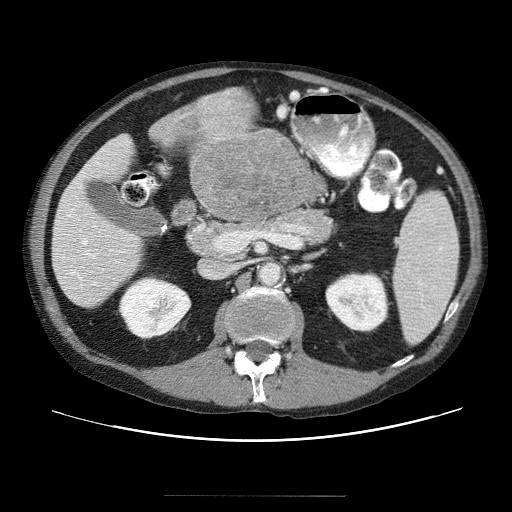
Contrast-enhanced abdominal CT (liver protocol), one axial slice; slice 13 of 69 in the series (ordered by position); 120 kVp; soft-tissue window (W 400 / L 40 HU); 2.5 mm slice thickness; 512 × 512 image matrix. Case-level facts recorded for this patient, not image findings: diagnosis: hepatocellular carcinoma (patient treated with transarterial chemoembolisation; whether this scan precedes or follows treatment is not stated here); TNM stage (as recorded): Stage-IVB; Child-Pugh class: B.
Outlined on this slice (semi-automatically segmented with operator editing):
- liver parenchyma outside the tumour (the mass and vessels are separate outlines, so this box may not span the whole liver): bounding box [x1, y1, x2, y2] px = [52, 102, 310, 302]
- mass: [190, 133, 311, 225]
- liver vessels: [57, 211, 124, 293]